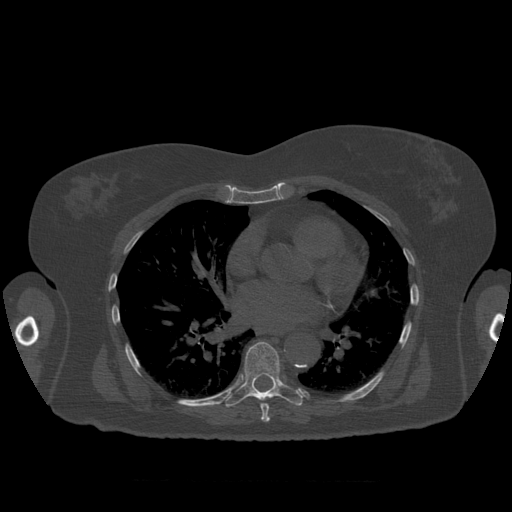
CT including the spine, one axial slice; position 383 of 399 along the scan axis; reconstruction kernel STANDARD; 120 kVp; bone window (W 1800 / L 400 HU); 512 × 512 image matrix. Patient age 81 years. Case-level facts recorded for this patient, not image findings: primary cancer: renal; vertebrae with lytic lesions (as recorded): L1.
Annotated regions visible in this slice (semi-automatic segmentation, software-assisted and operator-edited):
- T7 vertebra: bounding box (x1, y1, x2, y2) in pixels: (257, 398, 270, 422)
- T8 vertebra: (225, 342, 303, 408)